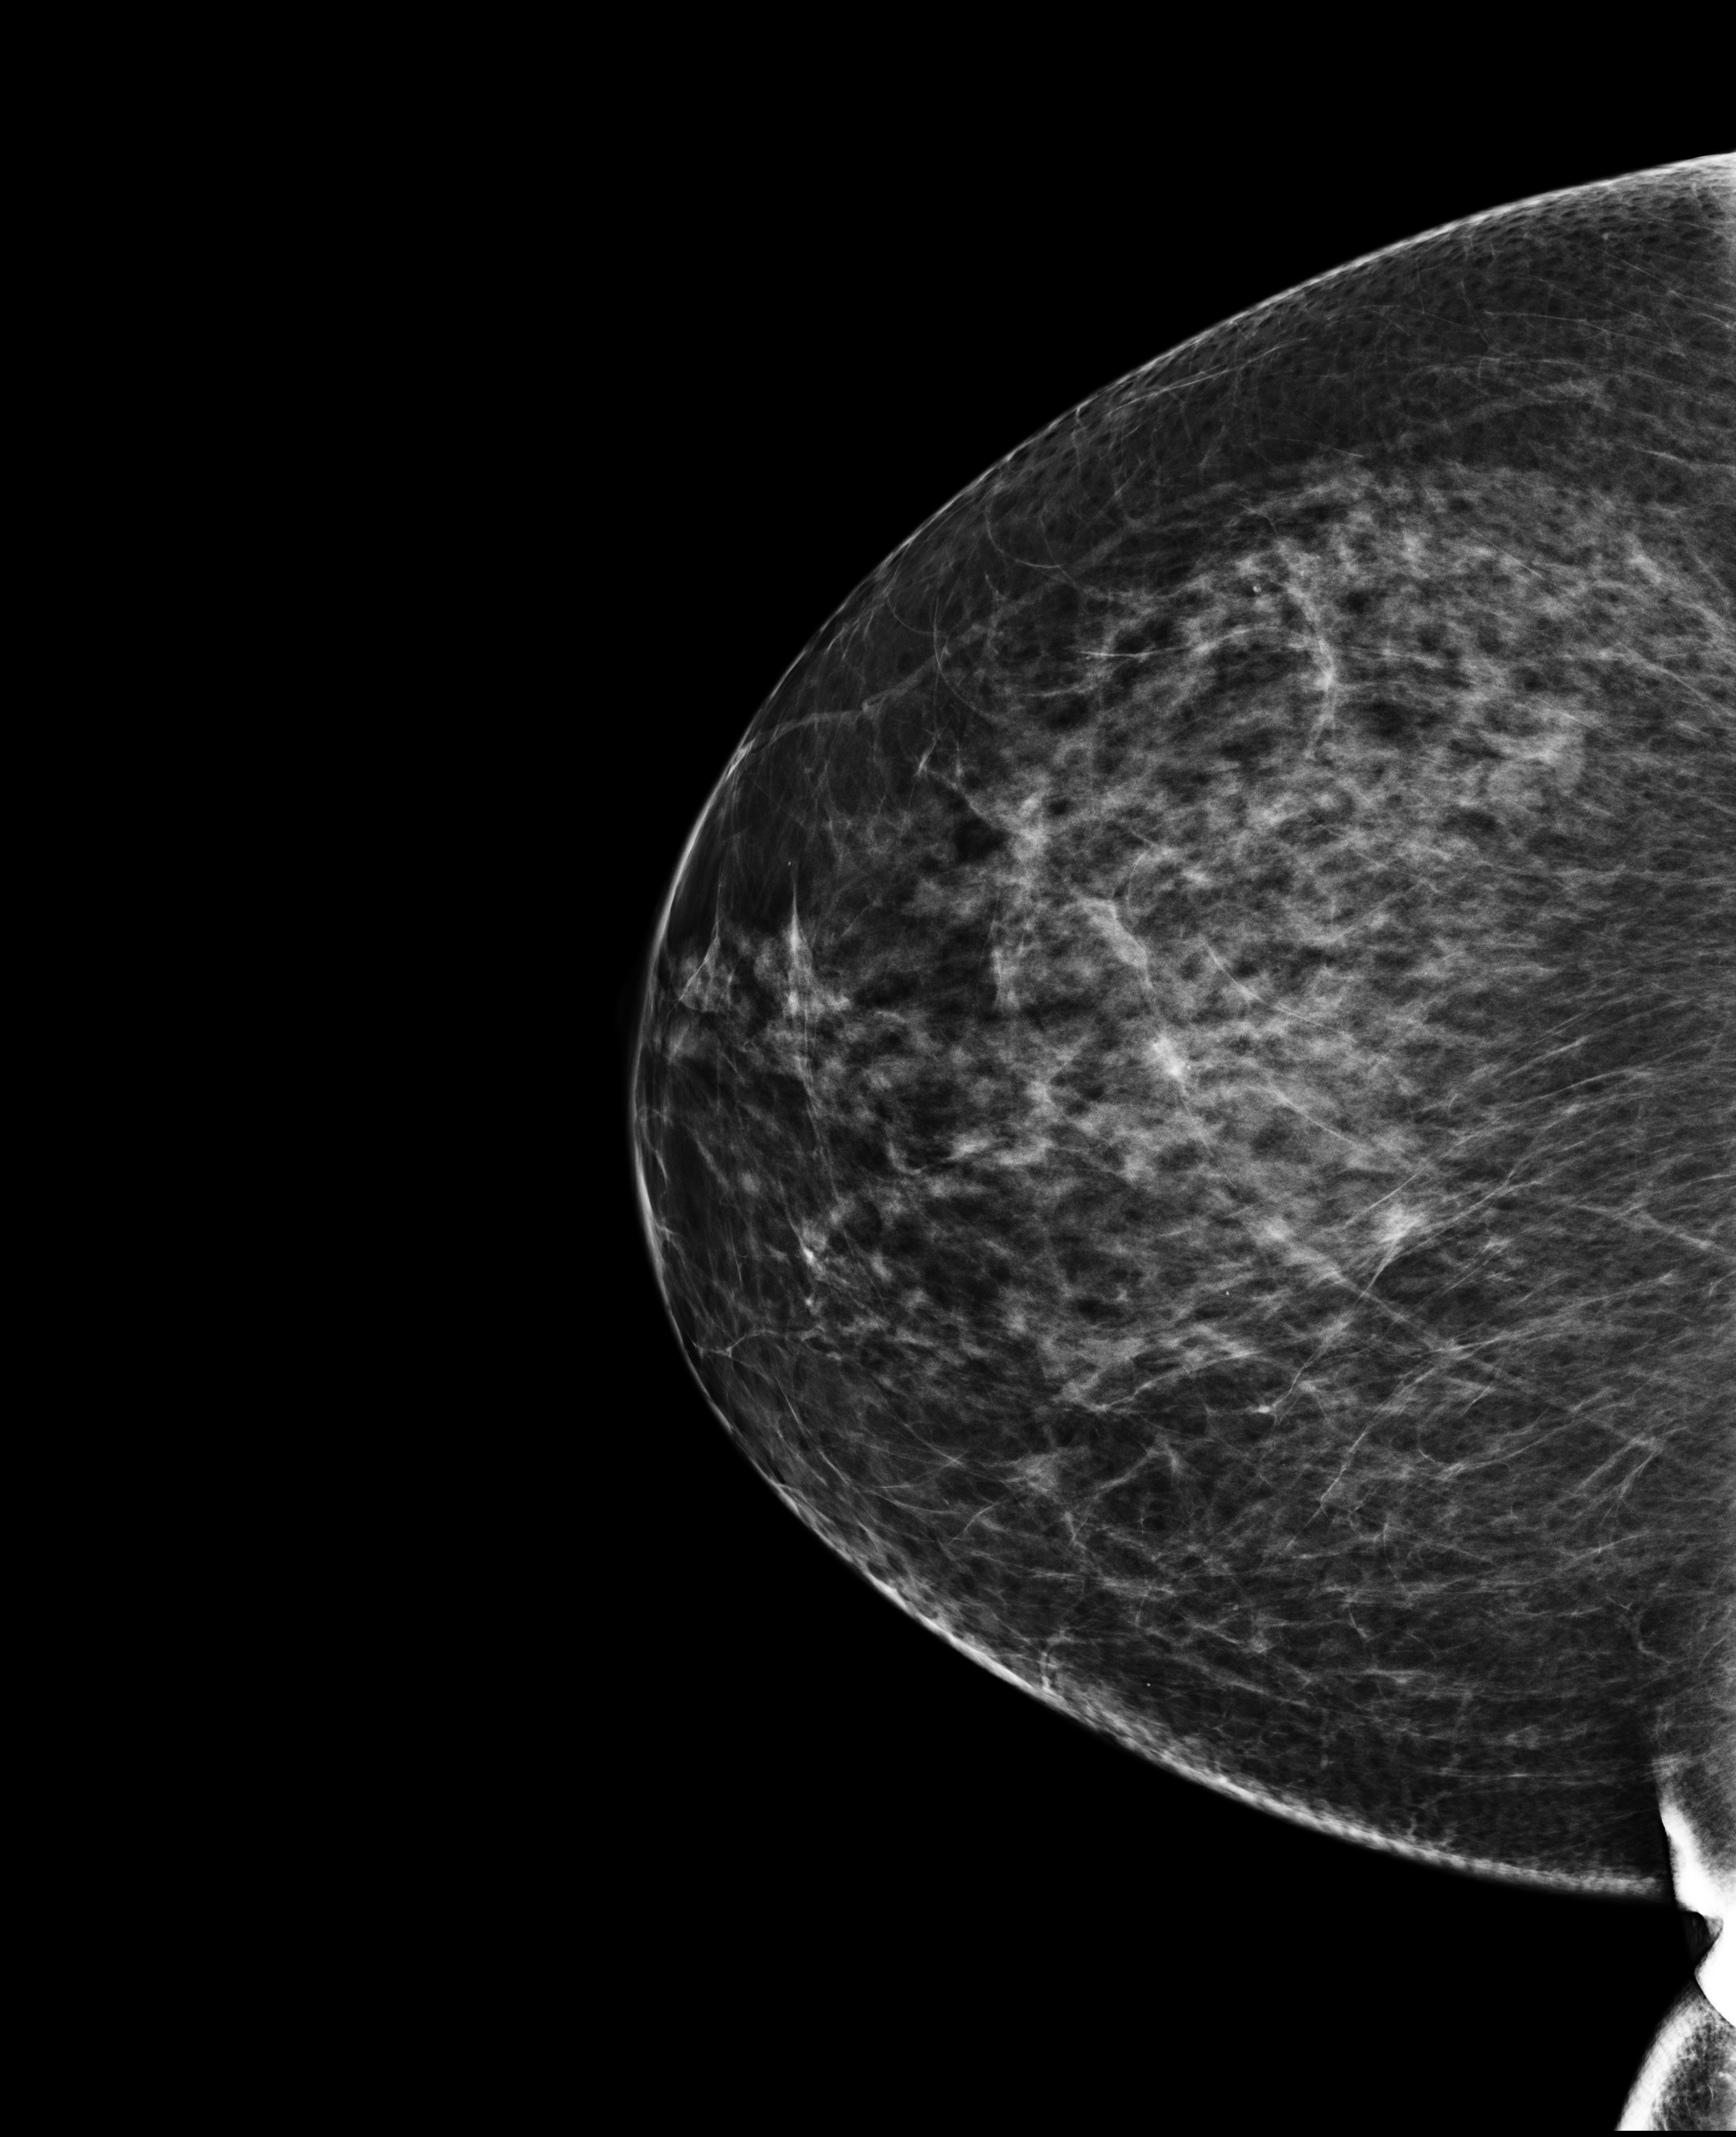
Full-field digital mammogram (FFDM); right breast; craniocaudal (CC) view; diagnostic examination (additional views). Patient aged 56 years (female).
- BI-RADS breast density category at the screening exam (both breasts, scale 1–4): 3
- final BI-RADS category for the screening round (tomosynthesis exam, both breasts): category 5
- recall: recalled for additional imaging after this screen